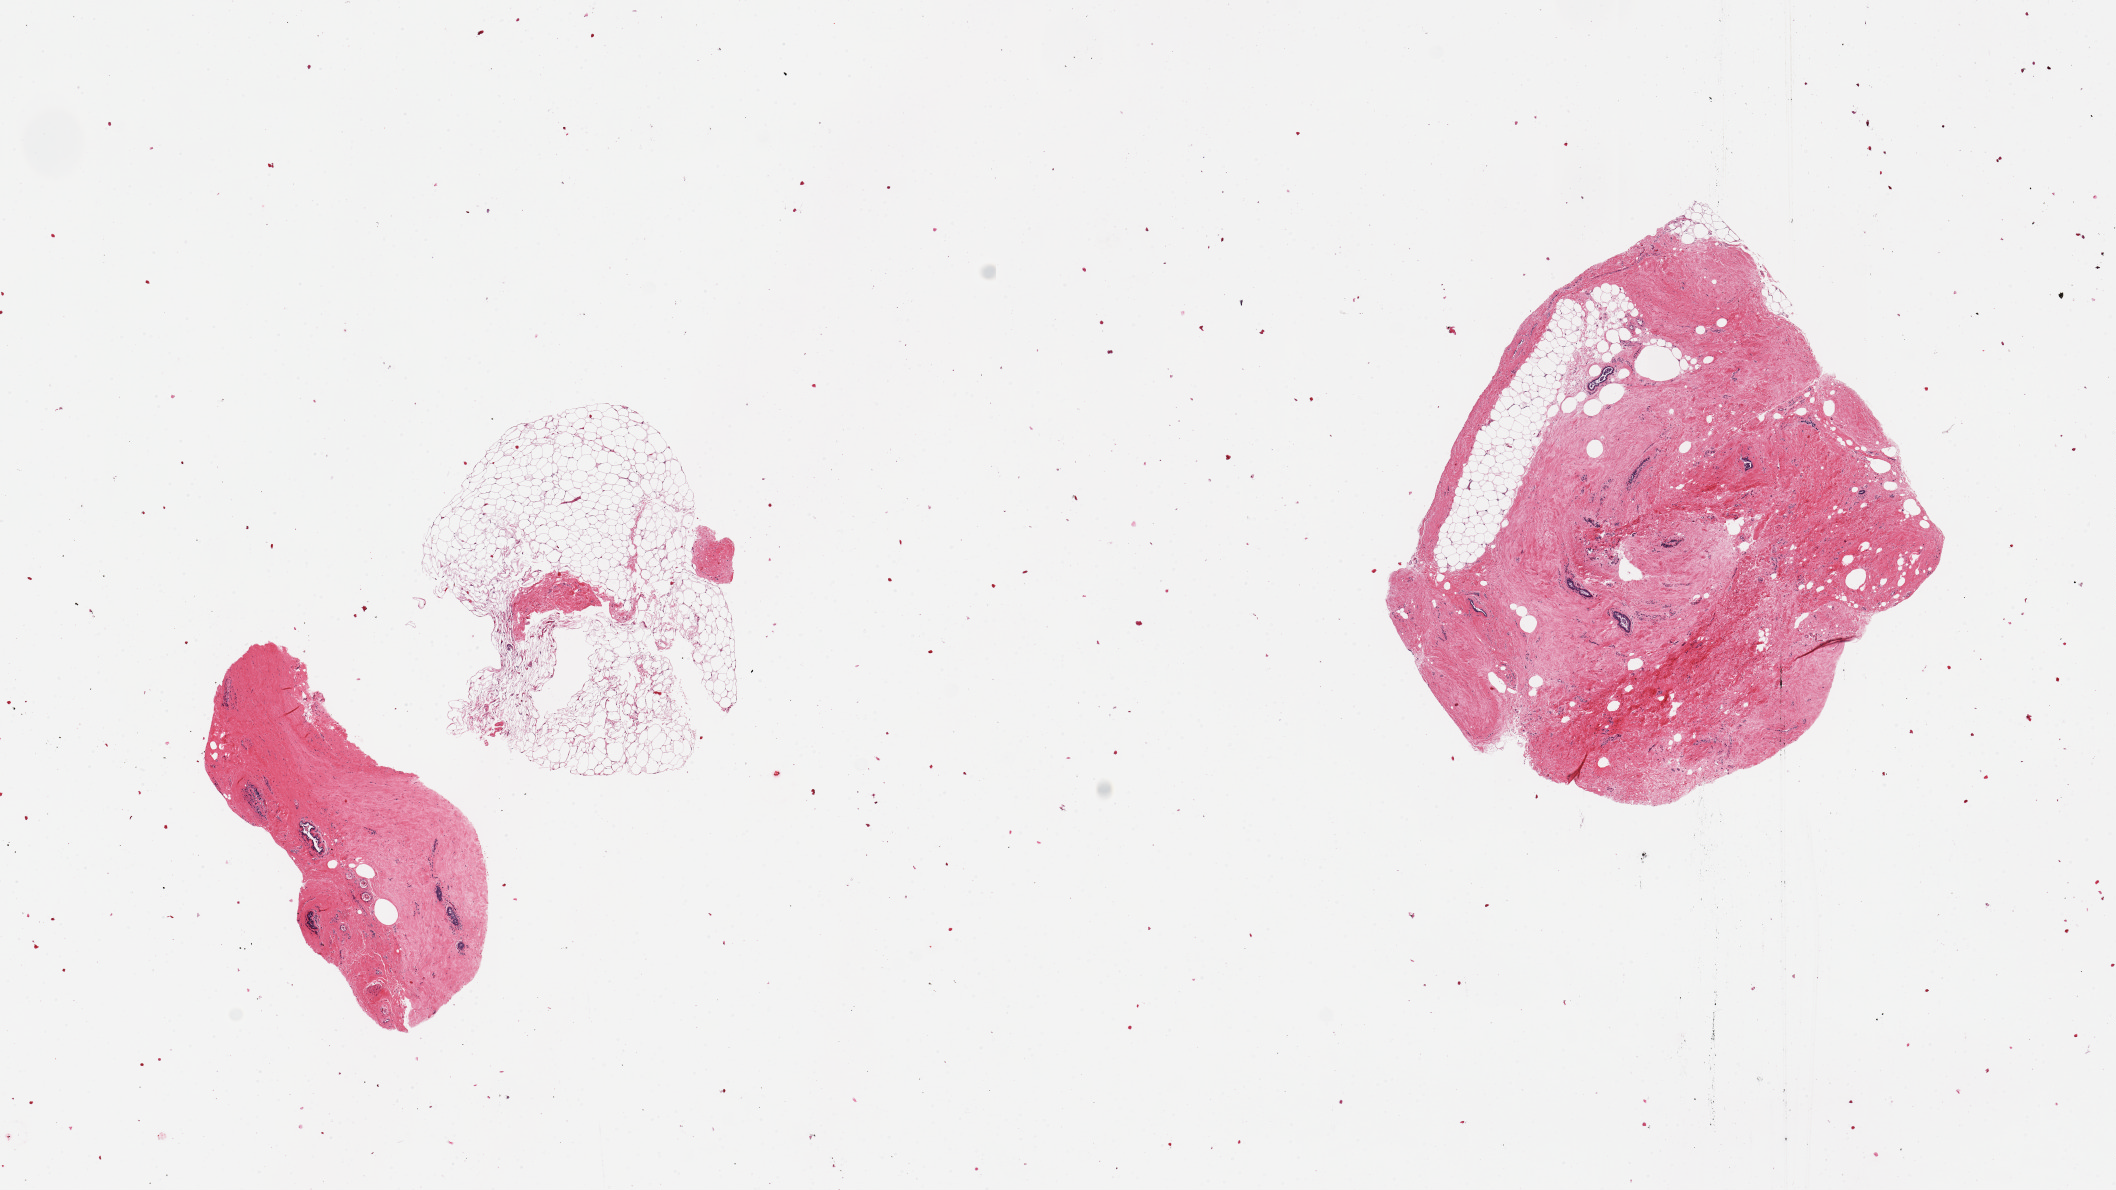
Hematoxylin and eosin (H&E) whole-slide image — whole scanned area (about 16.7 x 9.4 mm) shown as a low-resolution overview; PAXgene-fixed paraffin-embedded (PFPE) section; section of breast (target tissue); tissue donor sample. Donor sex: male.
Reviewer comment on this tissue sample: 3 pieces; one piece is fat, two are predominantly dense stroma with few ducts.